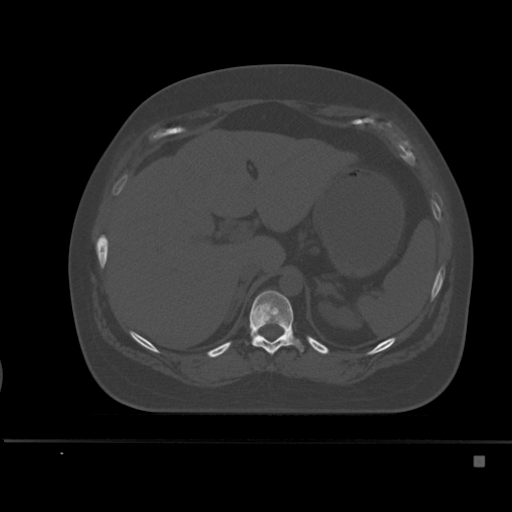
CT including the spine, one axial slice. Position 231 of 495 along the scan axis. Bone window (W 1800 / L 400 HU). 1.5 mm slice thickness. 512 × 512 image matrix. Patient: female, 33 years. From the clinical record (not read from this slice): primary cancer: breast.
Structures marked on this image (semi-automatic segmentation, software-assisted and operator-edited):
- T11 vertebra: bounding box [x1, y1, x2, y2] px = [249, 290, 304, 355]